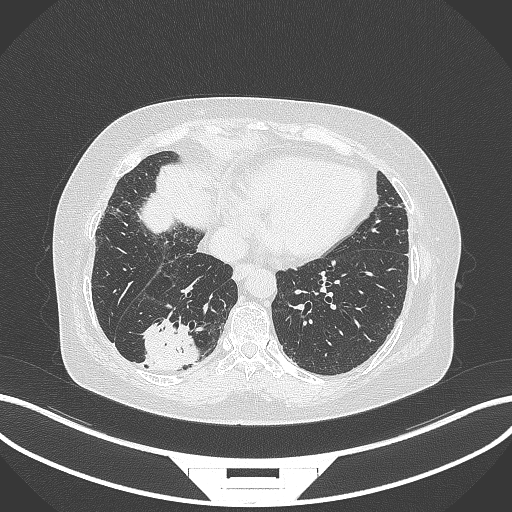
Chest CT, one axial slice. Slice 64 of 296 in the series (ordered by position). 120 kVp. Lung window (W 1500 / L -600 HU). 1 mm slice thickness. 512 × 512 image matrix, field of view 400 × 400 mm. Female patient, age 65 years. From the clinical record (not read from this slice): clinical TNM (as recorded): T2b N1 M0.
Annotated regions visible in this slice (rectangle marked by the reading radiologist):
- lung tumour (recorded histology: adenocarcinoma): bounding box [x1, y1, x2, y2] px = [136, 318, 200, 374]